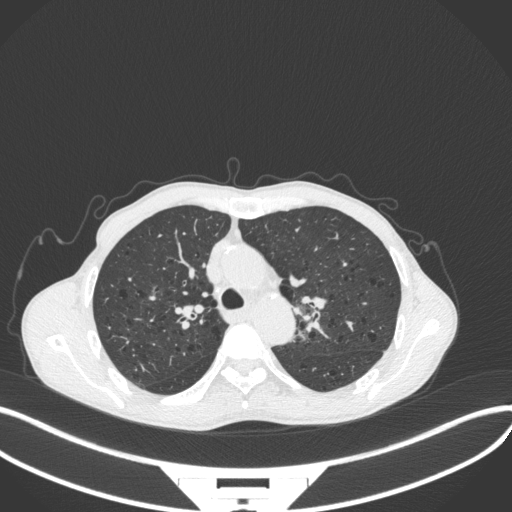
Chest CT, one axial slice; position 300 of 394 along the scan axis; reconstruction kernel B31f; 120 kVp; lung window (W 1500 / L -600 HU); 1 mm slice thickness; 512 × 512 image matrix, field of view 400 × 400 mm. Male patient, age 65 years. Case-level facts recorded for this patient, not image findings: clinical TNM (as recorded): T2b N0 M0.
Structures marked on this image (bounding box drawn by a radiologist):
- lung tumour (recorded histology: adenocarcinoma): box from (x=292, y=286) to (x=326, y=340) px